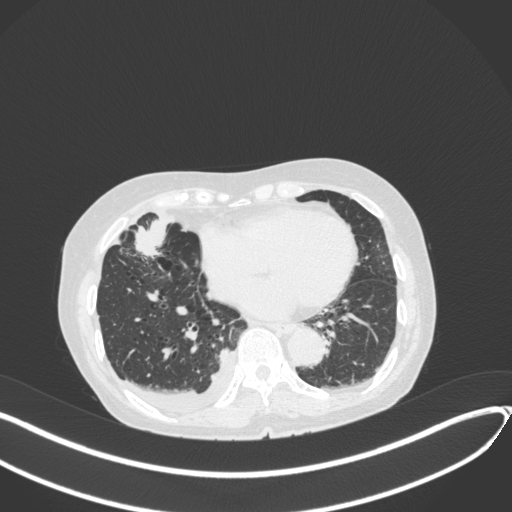
Chest CT, one axial slice; position 135 of 418 along the scan axis; reconstruction kernel B31f; 120 kVp; lung window (W 1500 / L -600 HU); 1 mm slice thickness; 512 × 512 image matrix, field of view 400 × 400 mm. Patient: female, 75 years. Case-level facts recorded for this patient, not image findings: clinical TNM (as recorded): T2a N3 M0.
Outlined on this slice (rectangle marked by the reading radiologist):
- lung tumour (recorded histology: adenocarcinoma): box from (x=132, y=214) to (x=175, y=261) px